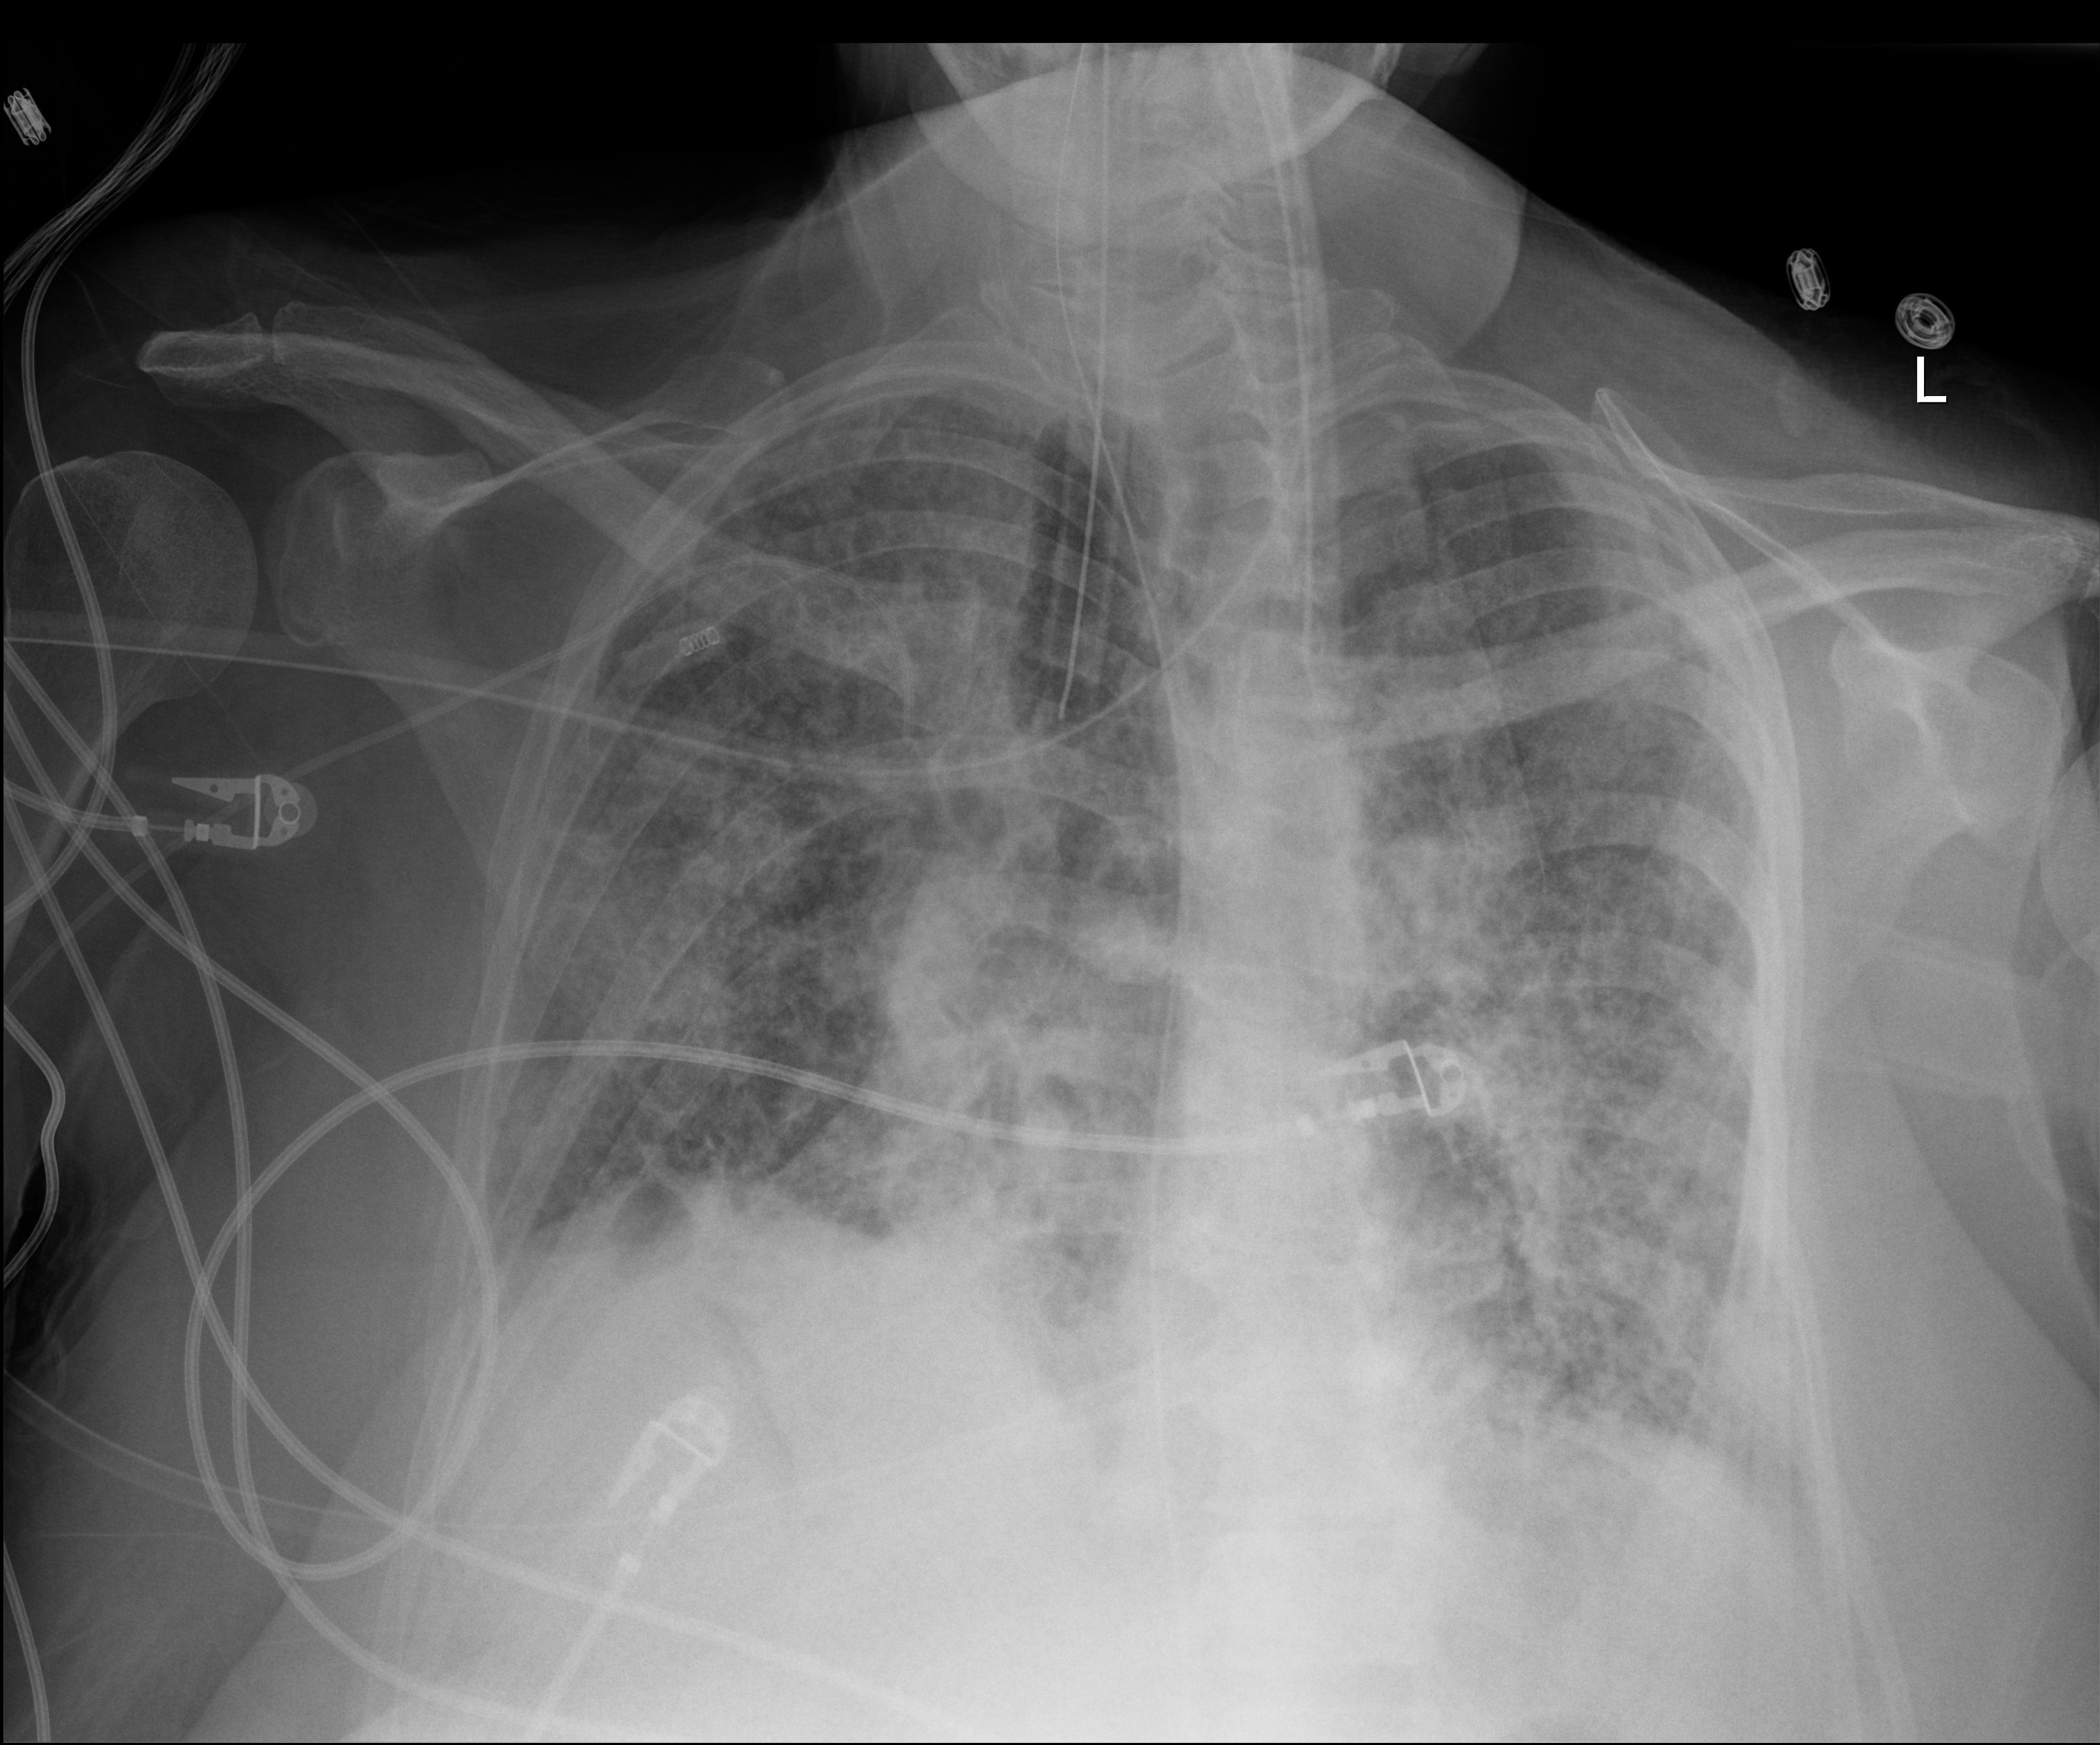
Chest X-ray (portable), anteroposterior (AP) projection. Patient hospitalised with COVID-19; female, aged 60–74 years.
Hospital-stay facts (about this admission, not read from this image; timing relative to this image not recorded): length of hospital stay: 45 days; admitted to intensive care during this hospital stay: yes.